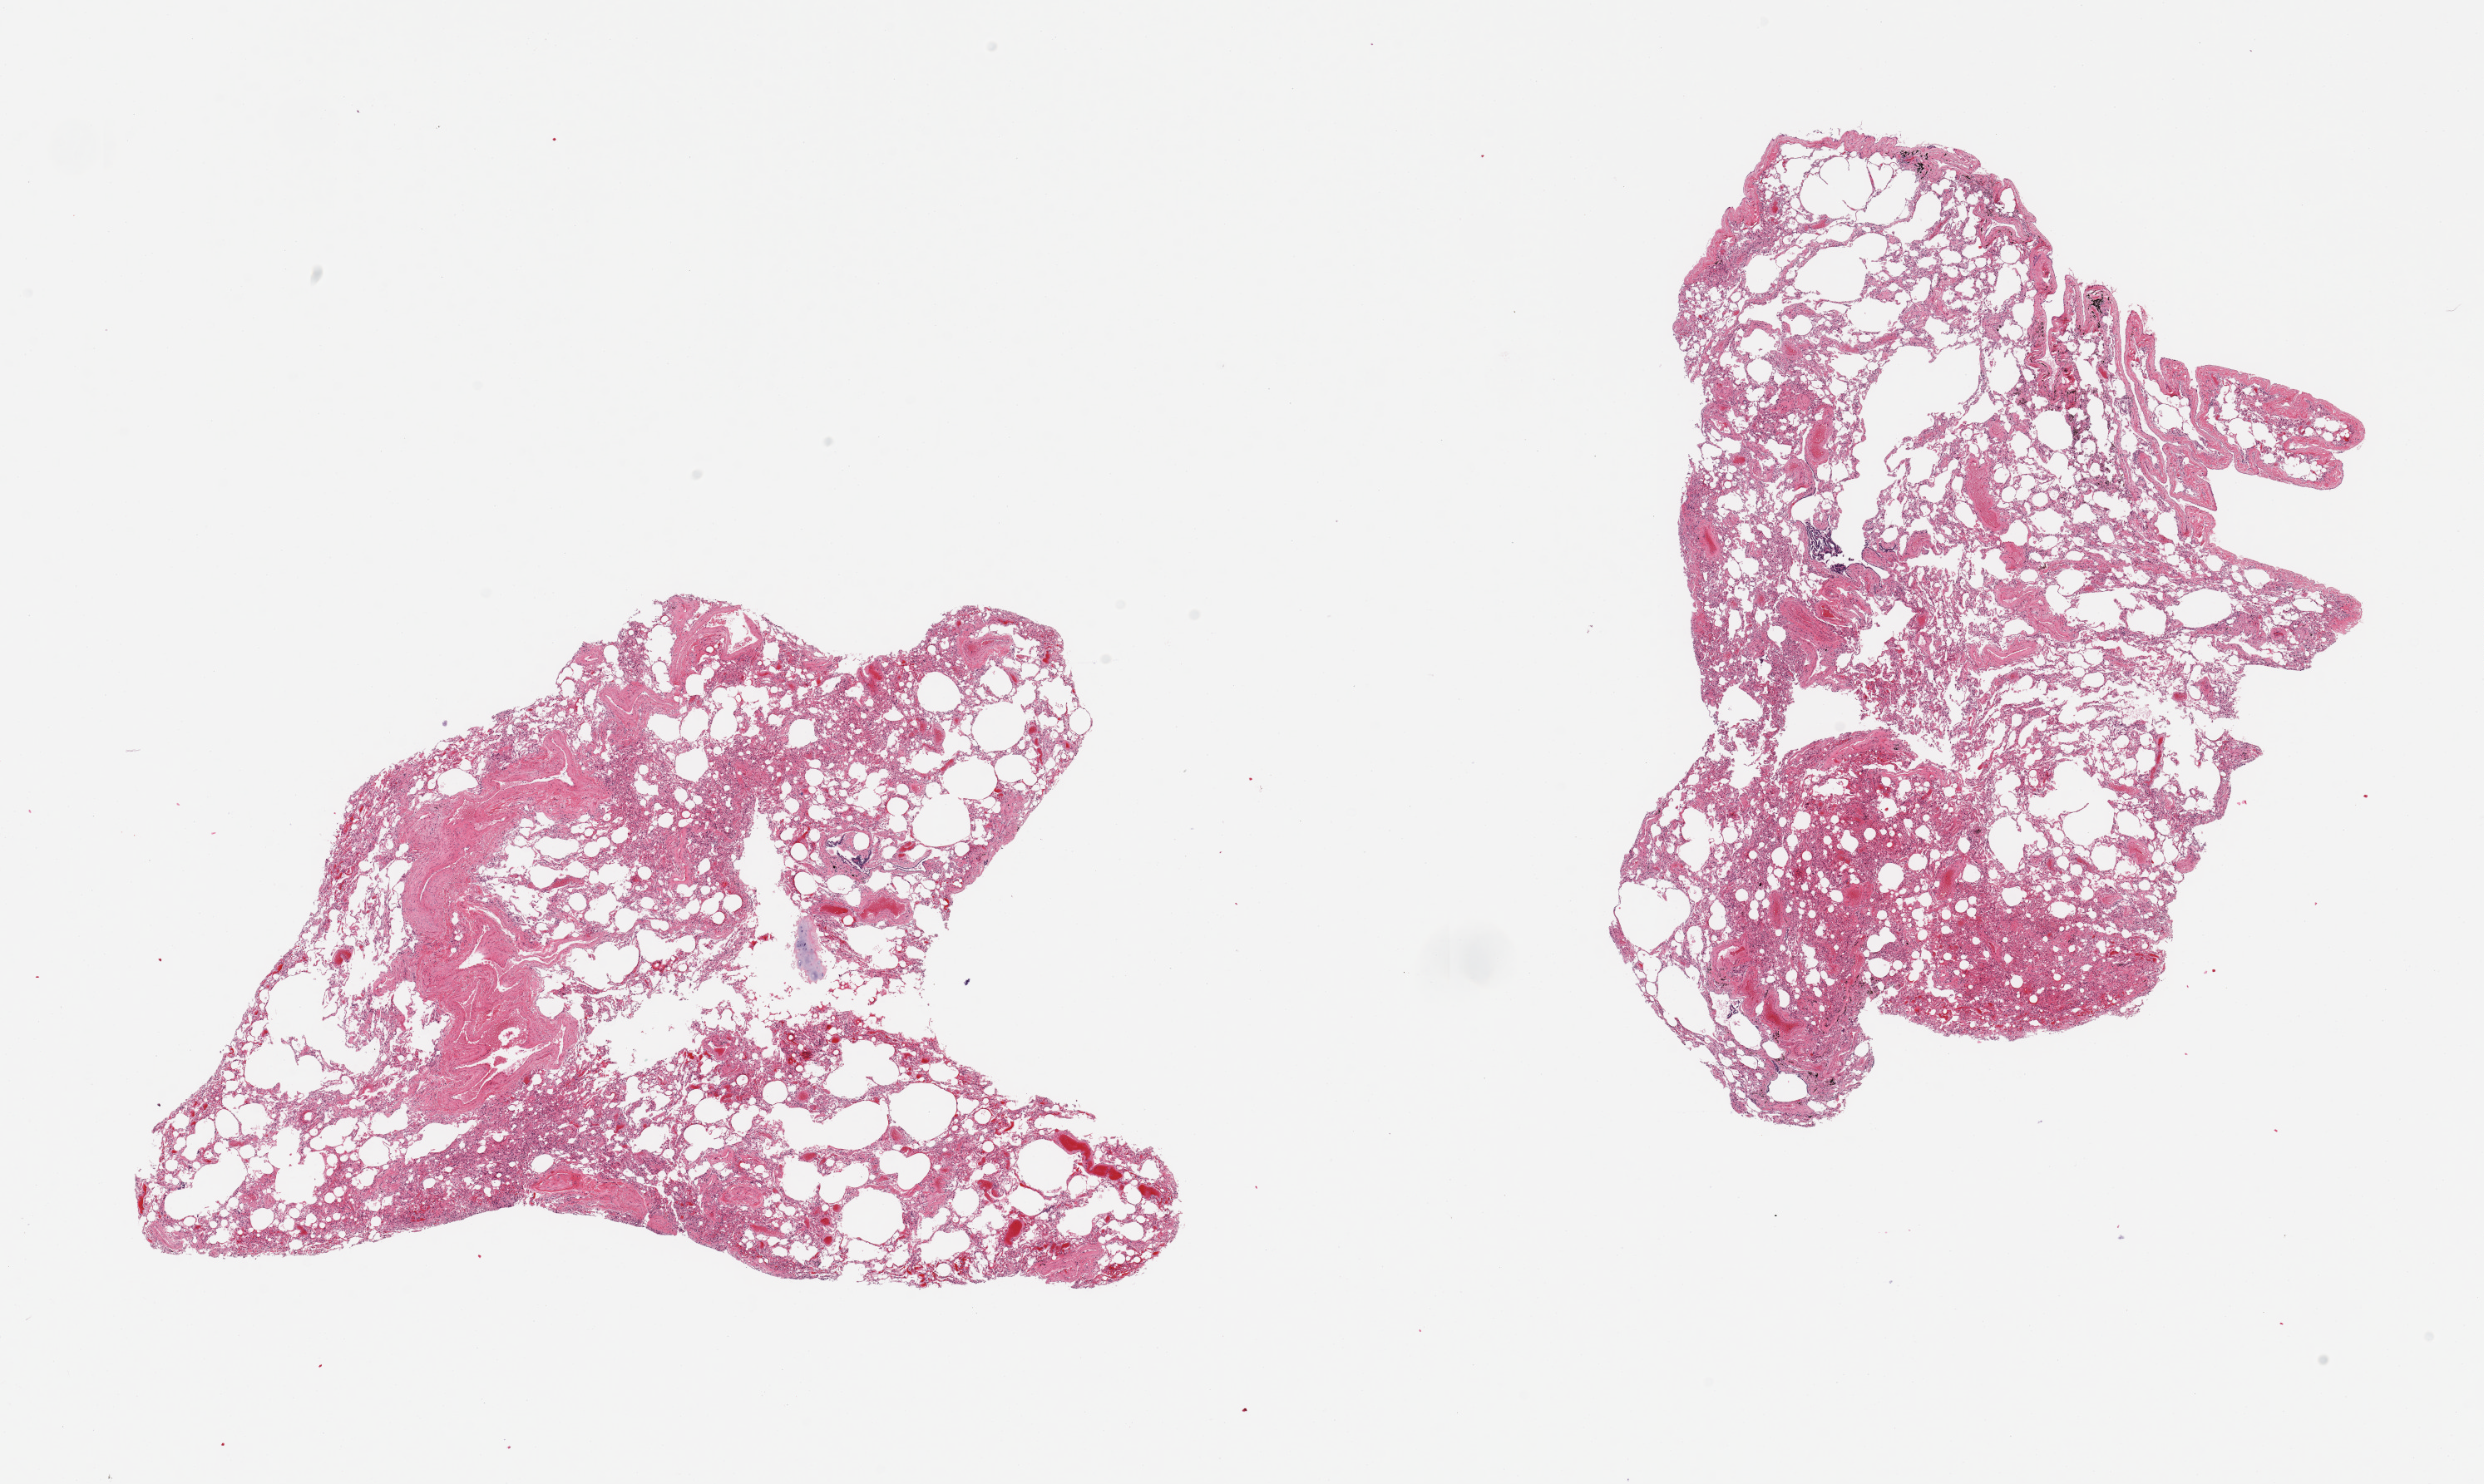
Digitized haematoxylin and eosin-stained section, brightfield, shown as a low-resolution overview of the whole scanned area (about 23.6 x 14.1 mm). PAXgene-fixed, paraffin-embedded tissue. Sampled site (target tissue): lung. Donor tissue sample. Donor sex: female.
Pathologist's review note for this sample: 2 pieces, moderate congestion.